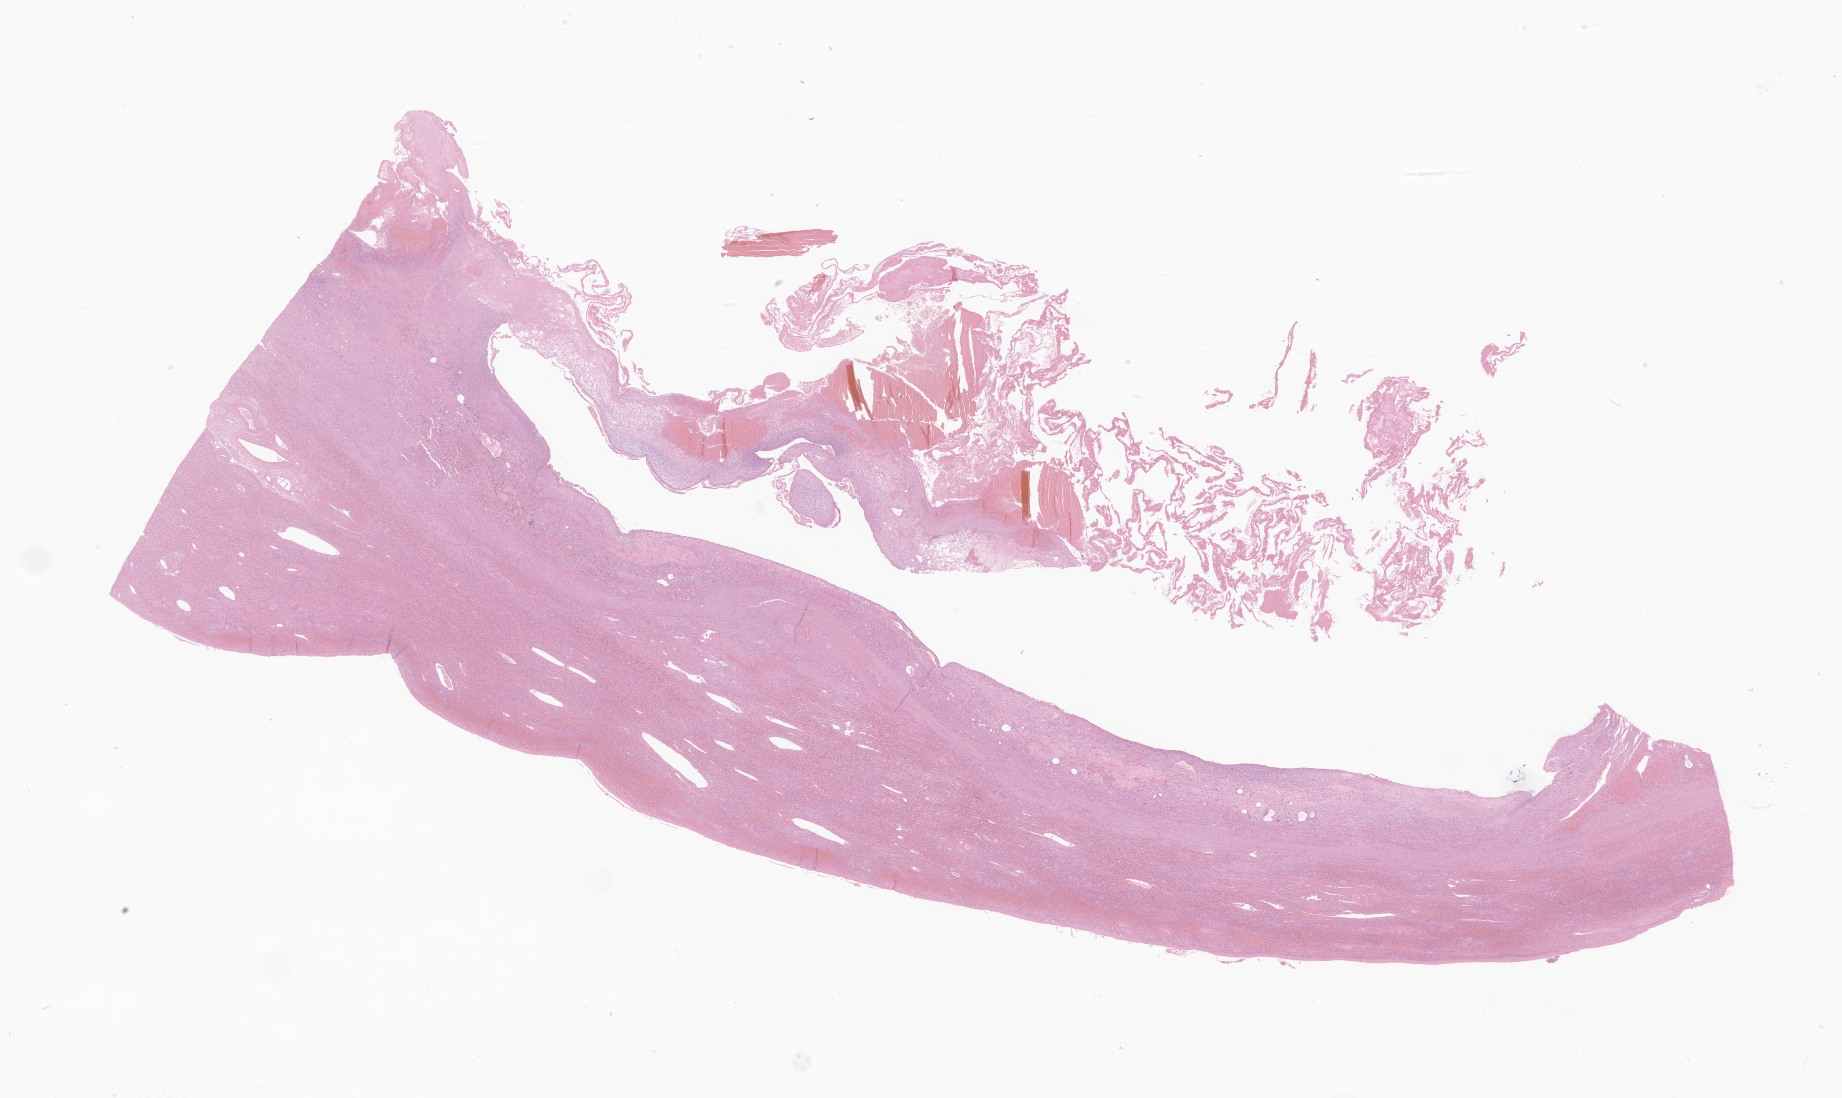
Hematoxylin and eosin (H&E) whole-slide image of tumor tissue from the liver — low-resolution overview of the scanned area, about 31.1 x 18.5 mm, formalin-fixed paraffin-embedded section. Female patient, age 143 months (11 years 11 months).
Recorded diagnosis: Embryonal sarcoma.